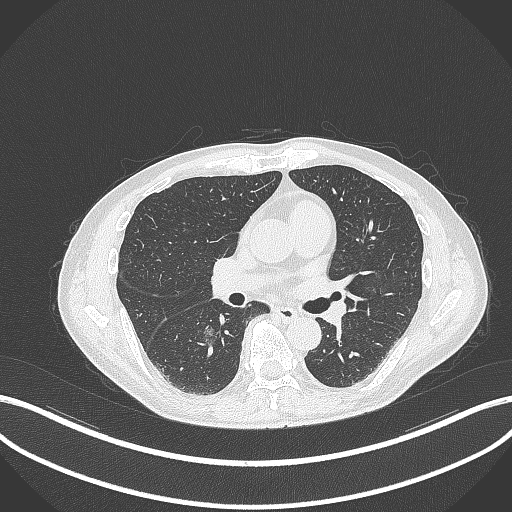
Chest CT, one axial slice. Position 173 of 323 along the scan axis. Reconstruction kernel B70f. 120 kVp. Lung window (W 1500 / L -600 HU). 512 × 512 image matrix. Male patient, age 61 years. Case-level facts recorded for this patient, not image findings: clinical TNM (as recorded): T1c N0 M0.
Annotated regions visible in this slice (bounding box drawn by a radiologist):
- lung tumour (recorded histology: adenocarcinoma): bounding box [x1, y1, x2, y2] px = [201, 325, 223, 346]